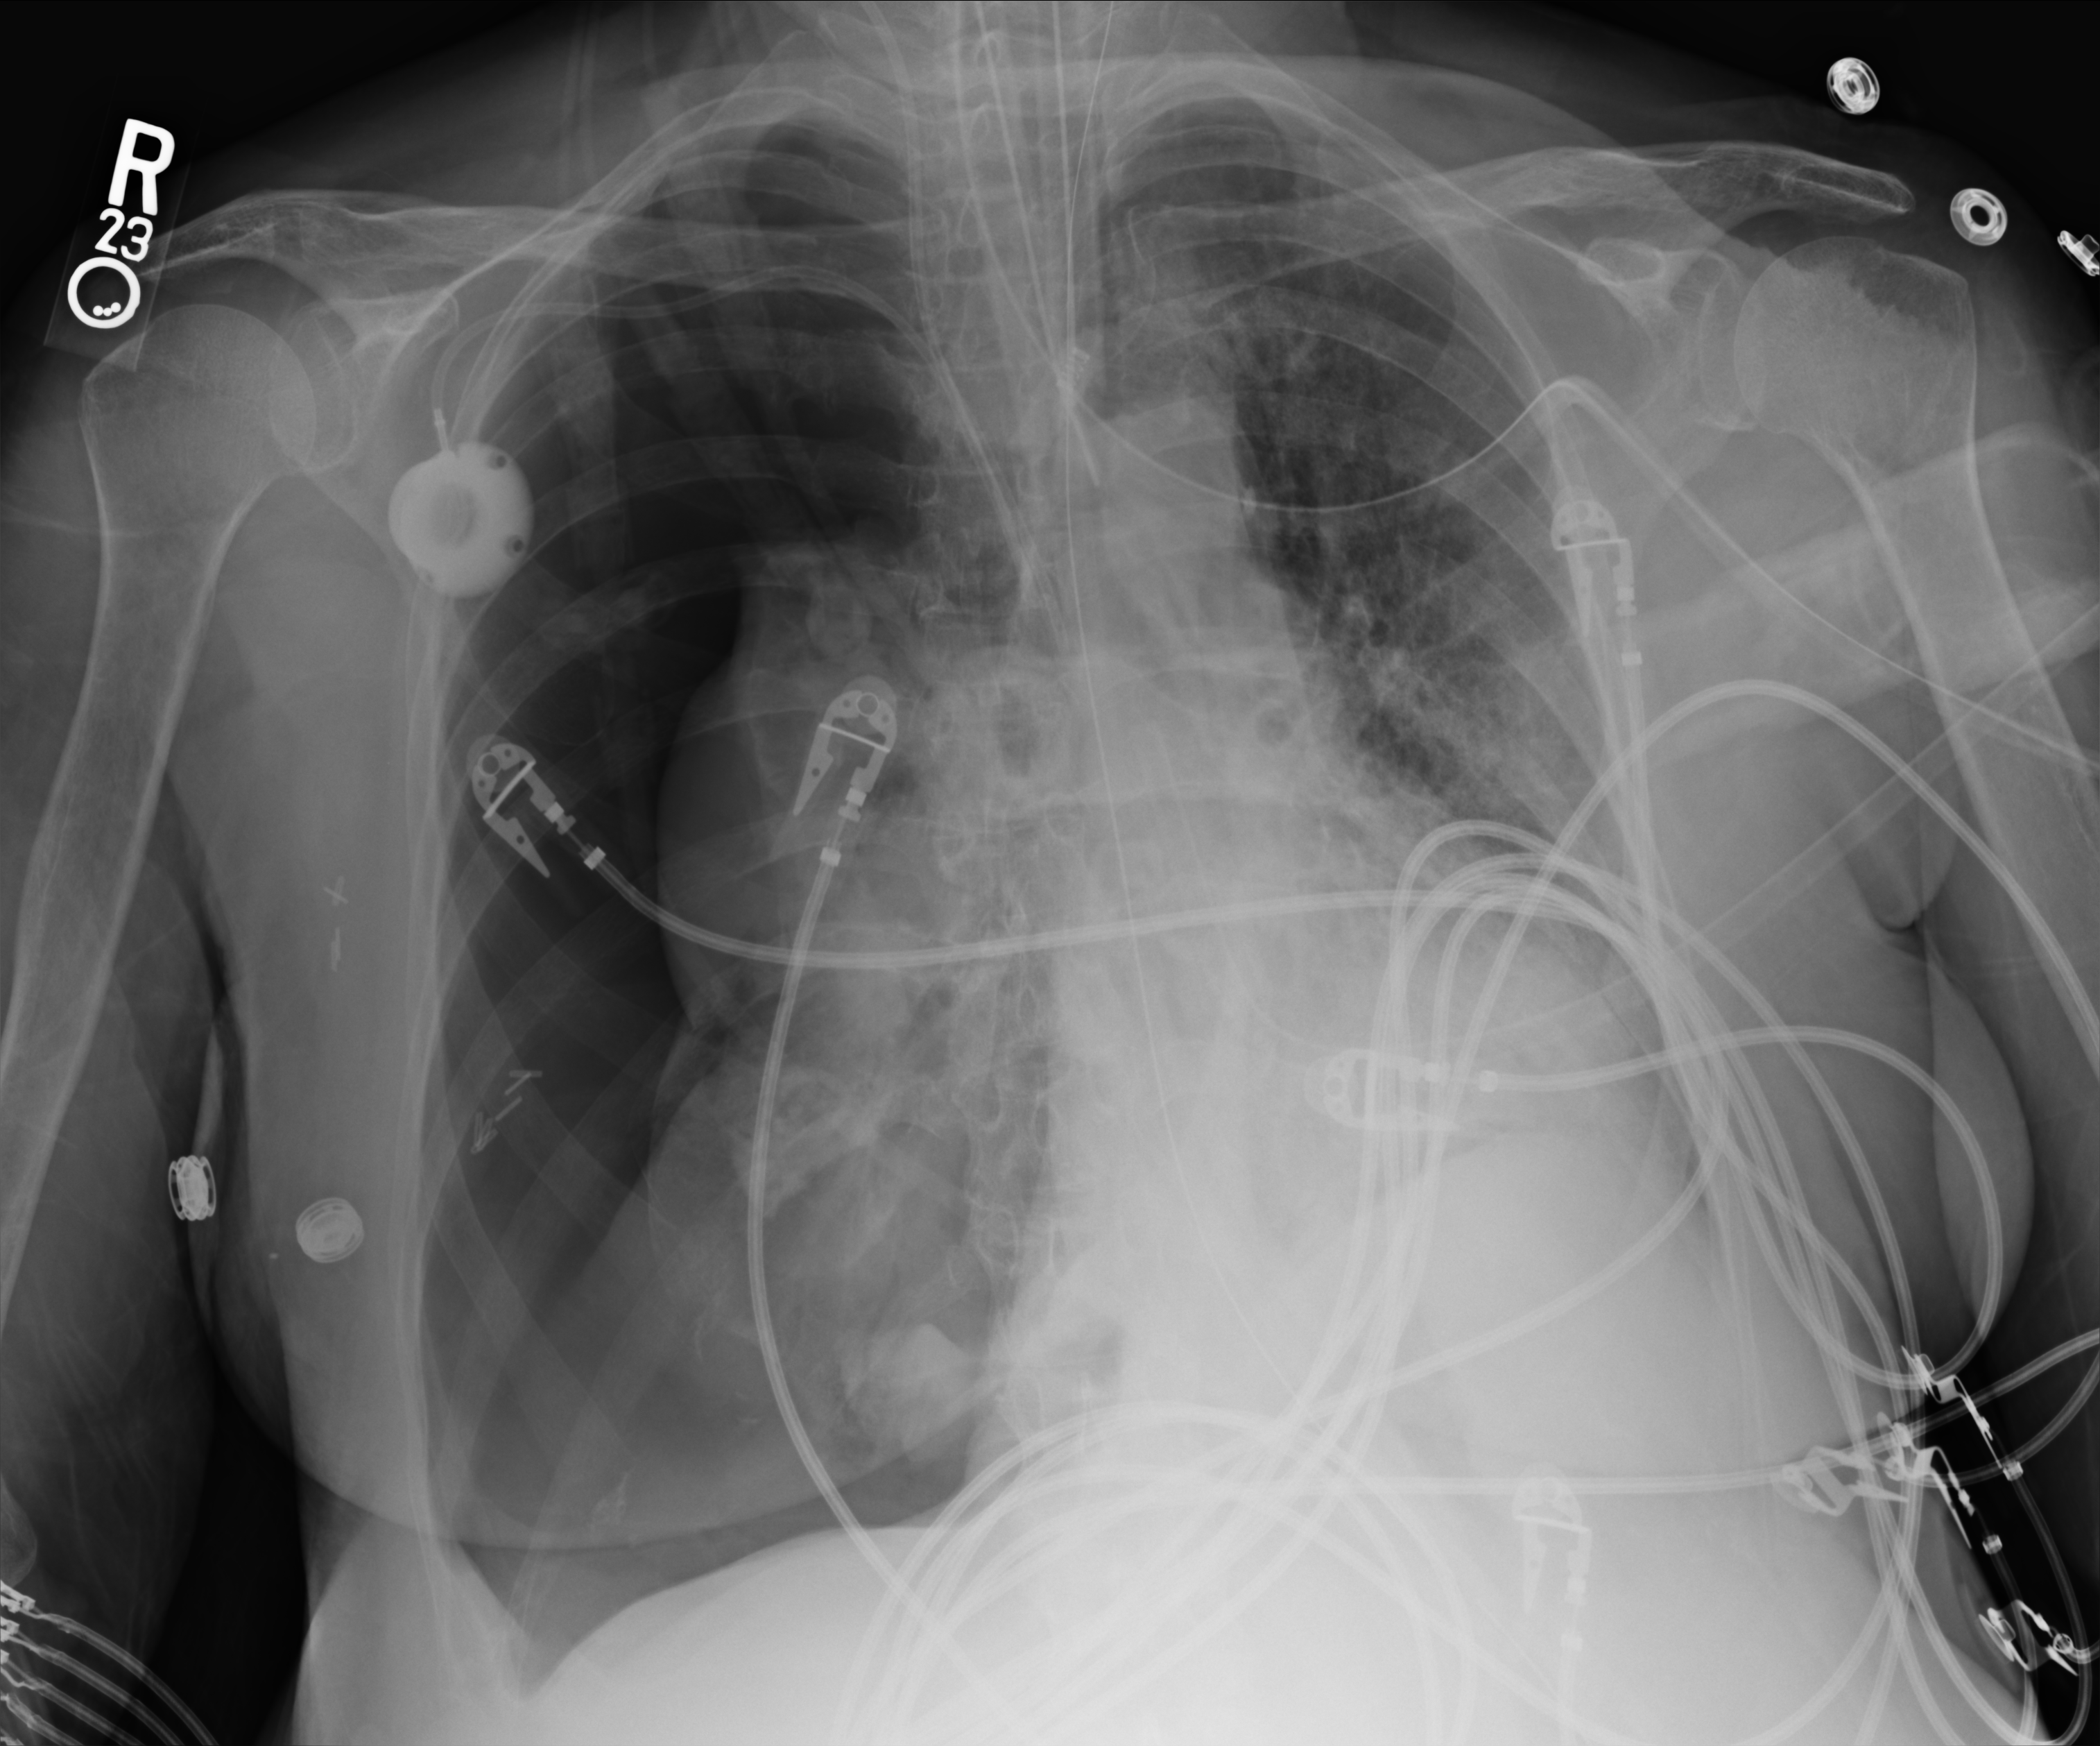
Chest X-ray (portable), anteroposterior (AP) projection. Female patient hospitalised with COVID-19, age 60–74 years.
From the hospital-stay record, not from the radiograph (when in the stay this image was taken is not recorded):
- COPD (admission record): no
- admitted to intensive care during this hospital stay: yes
- length of hospital stay: 43 days